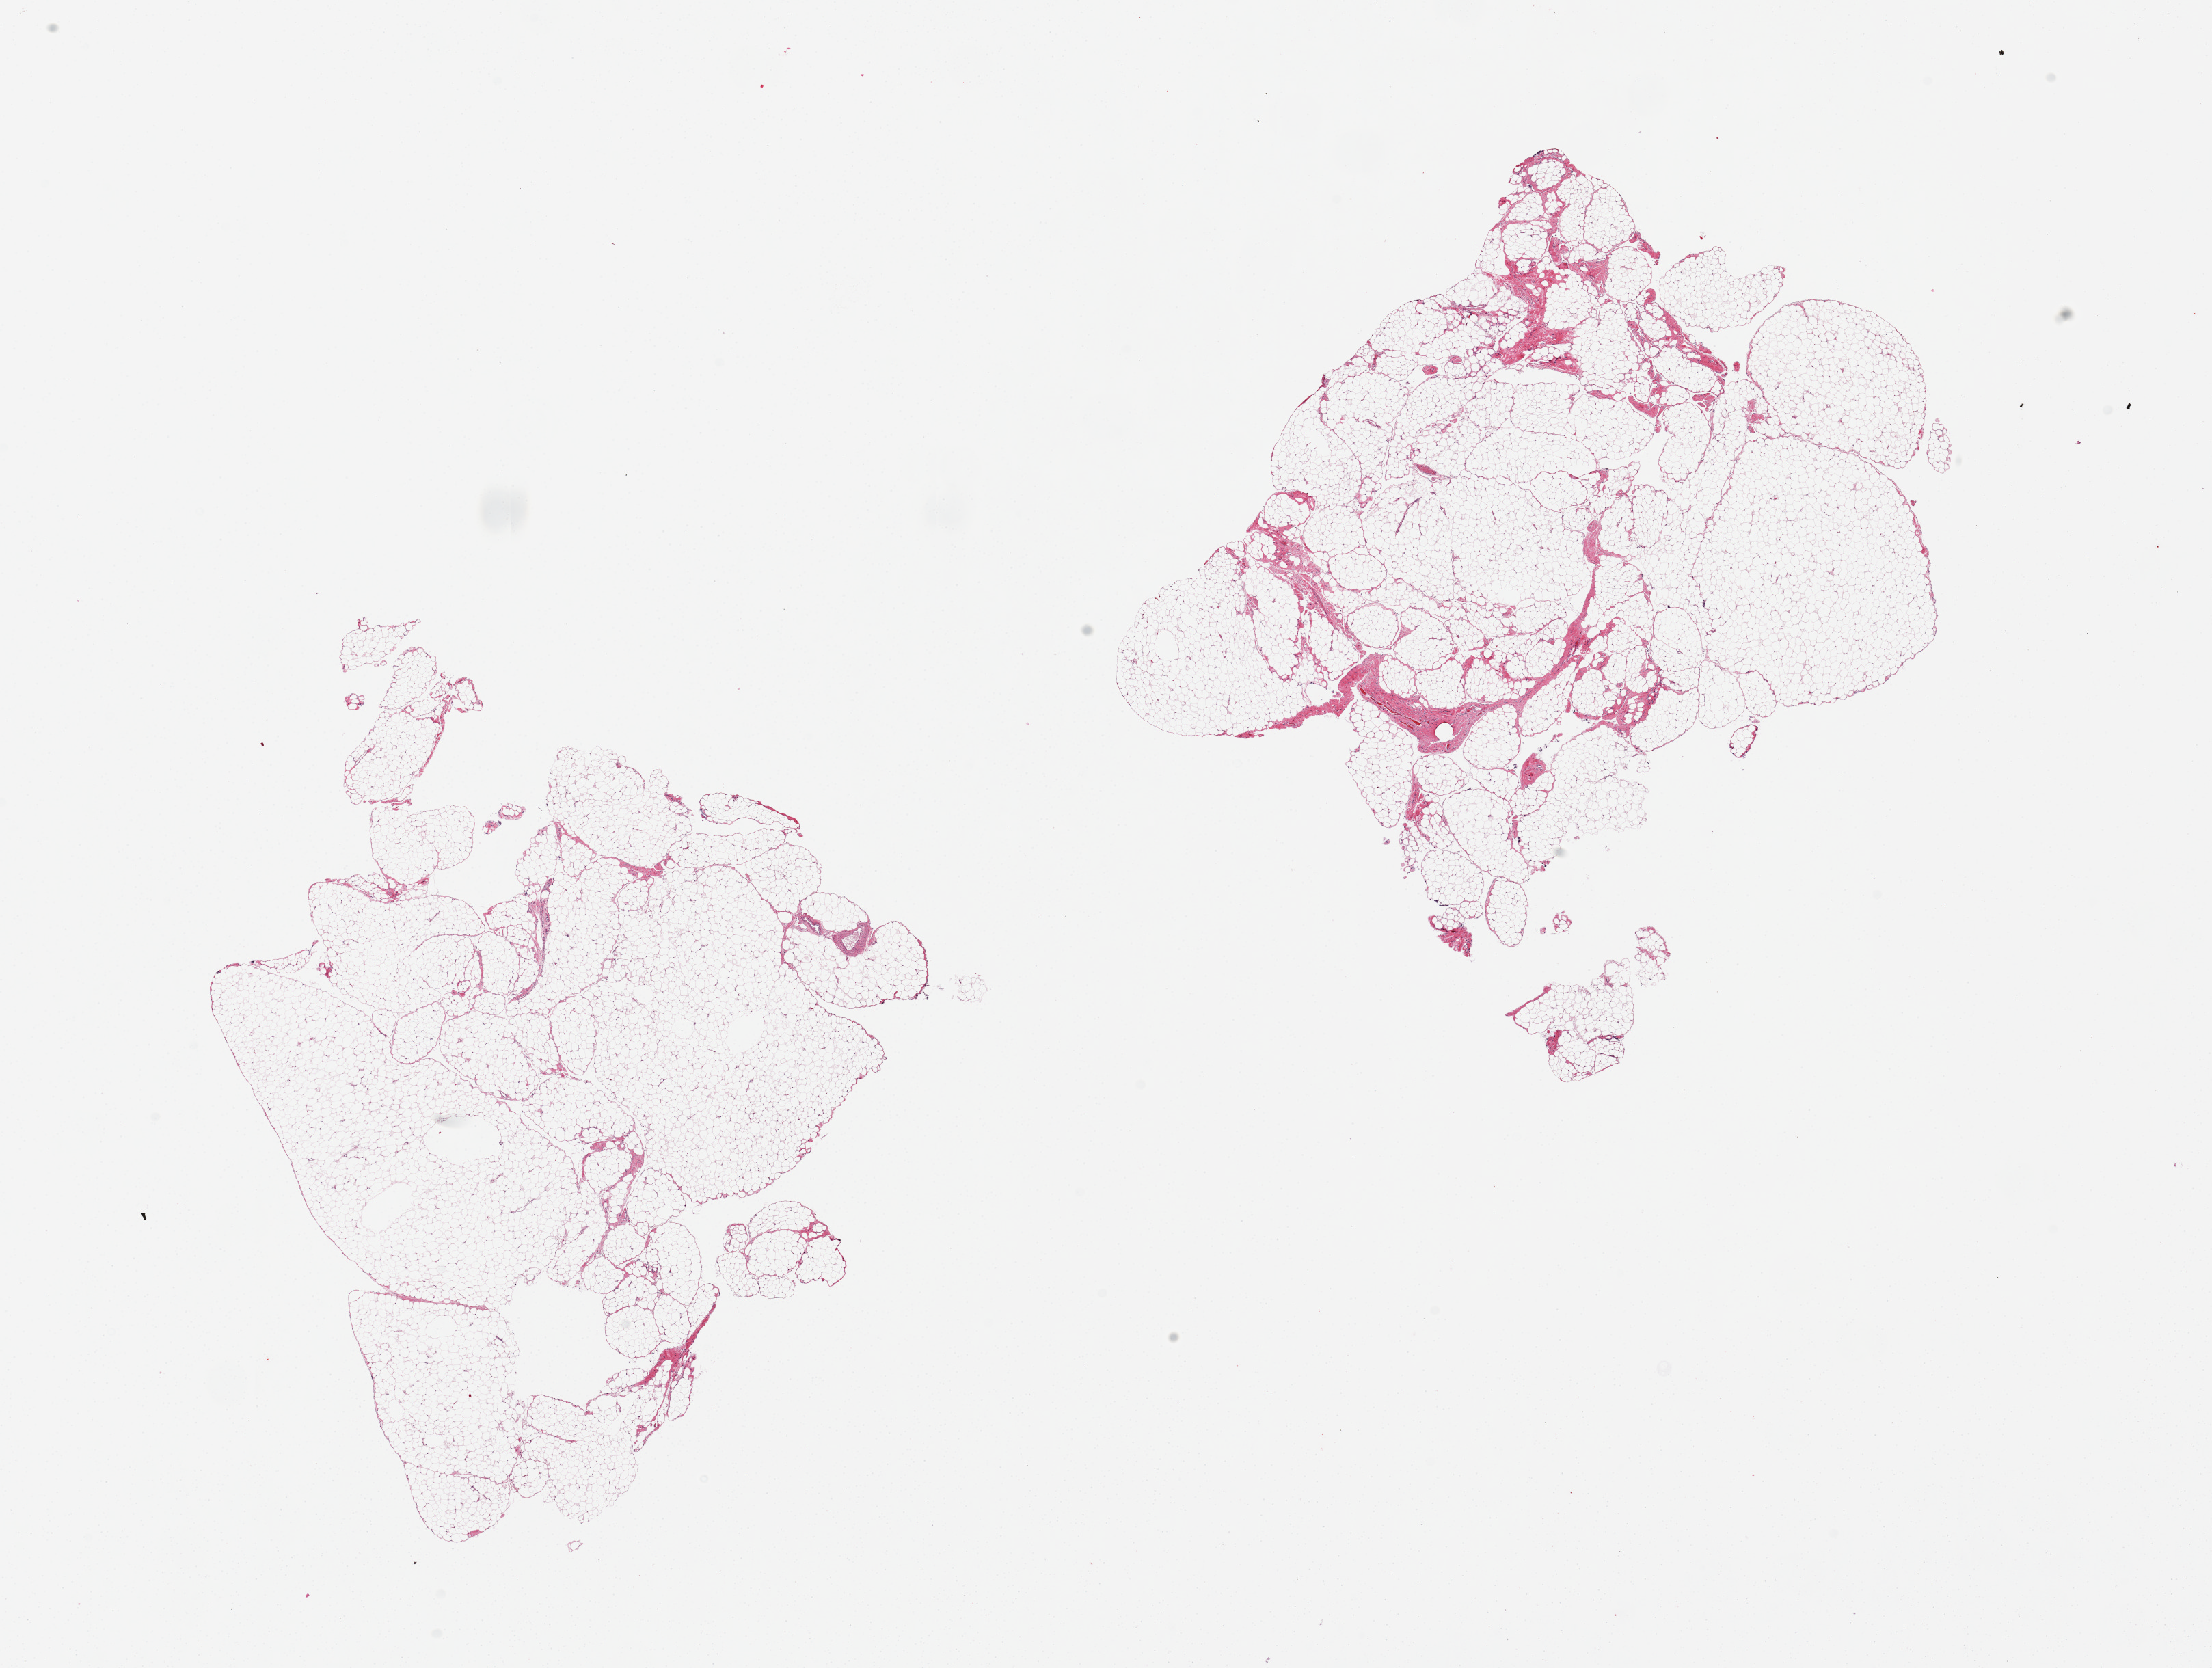
Whole-slide image, H&E stain, brightfield, low-resolution overview of the scanned area, about 25.6 x 19.3 mm, PAXgene-fixed paraffin-embedded (PFPE) section, target tissue: omentum, donor tissue sample. Donor: male.
Review note (as recorded): 2 pieces, both 8x7mm; ~10% fibrous tissue.